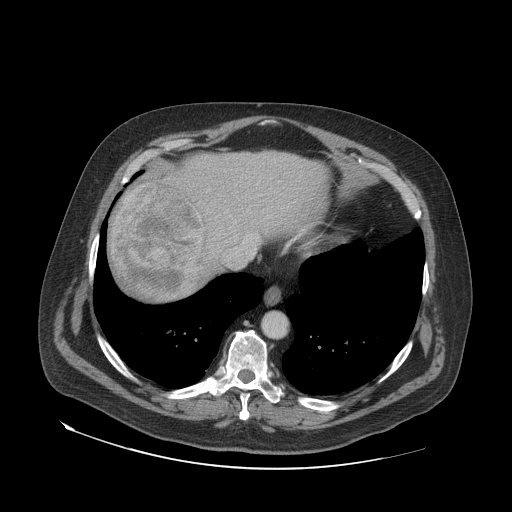
Contrast-enhanced abdominal CT (liver protocol), one axial slice; position 65 of 79 along the scan axis; reconstruction kernel STANDARD; 140 kVp; soft-tissue window (W 400 / L 40 HU); 2.5 mm slice thickness; 512 × 512 image matrix, field of view 480 × 480 mm. Case-level facts recorded for this patient, not image findings: diagnosis: hepatocellular carcinoma (patient treated with transarterial chemoembolisation; whether this scan precedes or follows treatment is not stated here); TNM stage (as recorded): Stage-IVA; Child-Pugh class: A; tumour differentiation: well differentiated; tumour nodularity: multinodular.
Outlined on this slice (semi-automatically segmented with operator editing):
- abdominal aorta: bounding box <262,313,286,338> (left, top, right, bottom; pixels)
- liver parenchyma outside the tumour (the mass and vessels are separate outlines, so this box may not span the whole liver): <108,150,328,300>
- mass: <113,182,205,296>